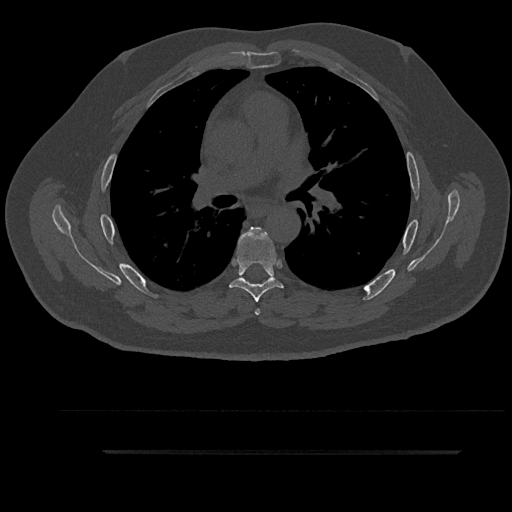
CT including the spine, one axial slice; position 583 of 797 along the scan axis; reconstruction kernel Br40s/3; 120 kVp; bone window (W 1800 / L 400 HU); 0.5 mm slice thickness; 512 × 512 image matrix, field of view 432 × 432 mm. Male patient, age 63 years. From the clinical record (not read from this slice): primary cancer: renal.
Structures marked on this image (semi-automatic segmentation, software-assisted and operator-edited):
- T5 vertebra: bounding box (x1, y1, x2, y2) in pixels: (244, 227, 267, 315)
- T6 vertebra: (229, 228, 284, 302)